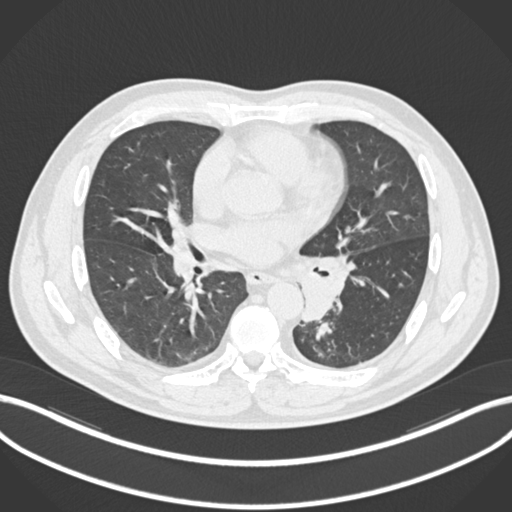
Chest CT, one axial slice. Position 111 of 223 along the scan axis. Reconstruction kernel B30f. Lung window (W 1500 / L -600 HU). 512 × 512 image matrix, field of view 400 × 400 mm. Patient: male, 50 years. Case-level facts recorded for this patient, not image findings: clinical TNM (as recorded): T2a N3 M0.
Outlined on this slice (bounding box drawn by a radiologist):
- lung tumour (recorded histology: squamous cell carcinoma): bounding box (x1, y1, x2, y2) in pixels: (296, 267, 349, 326)